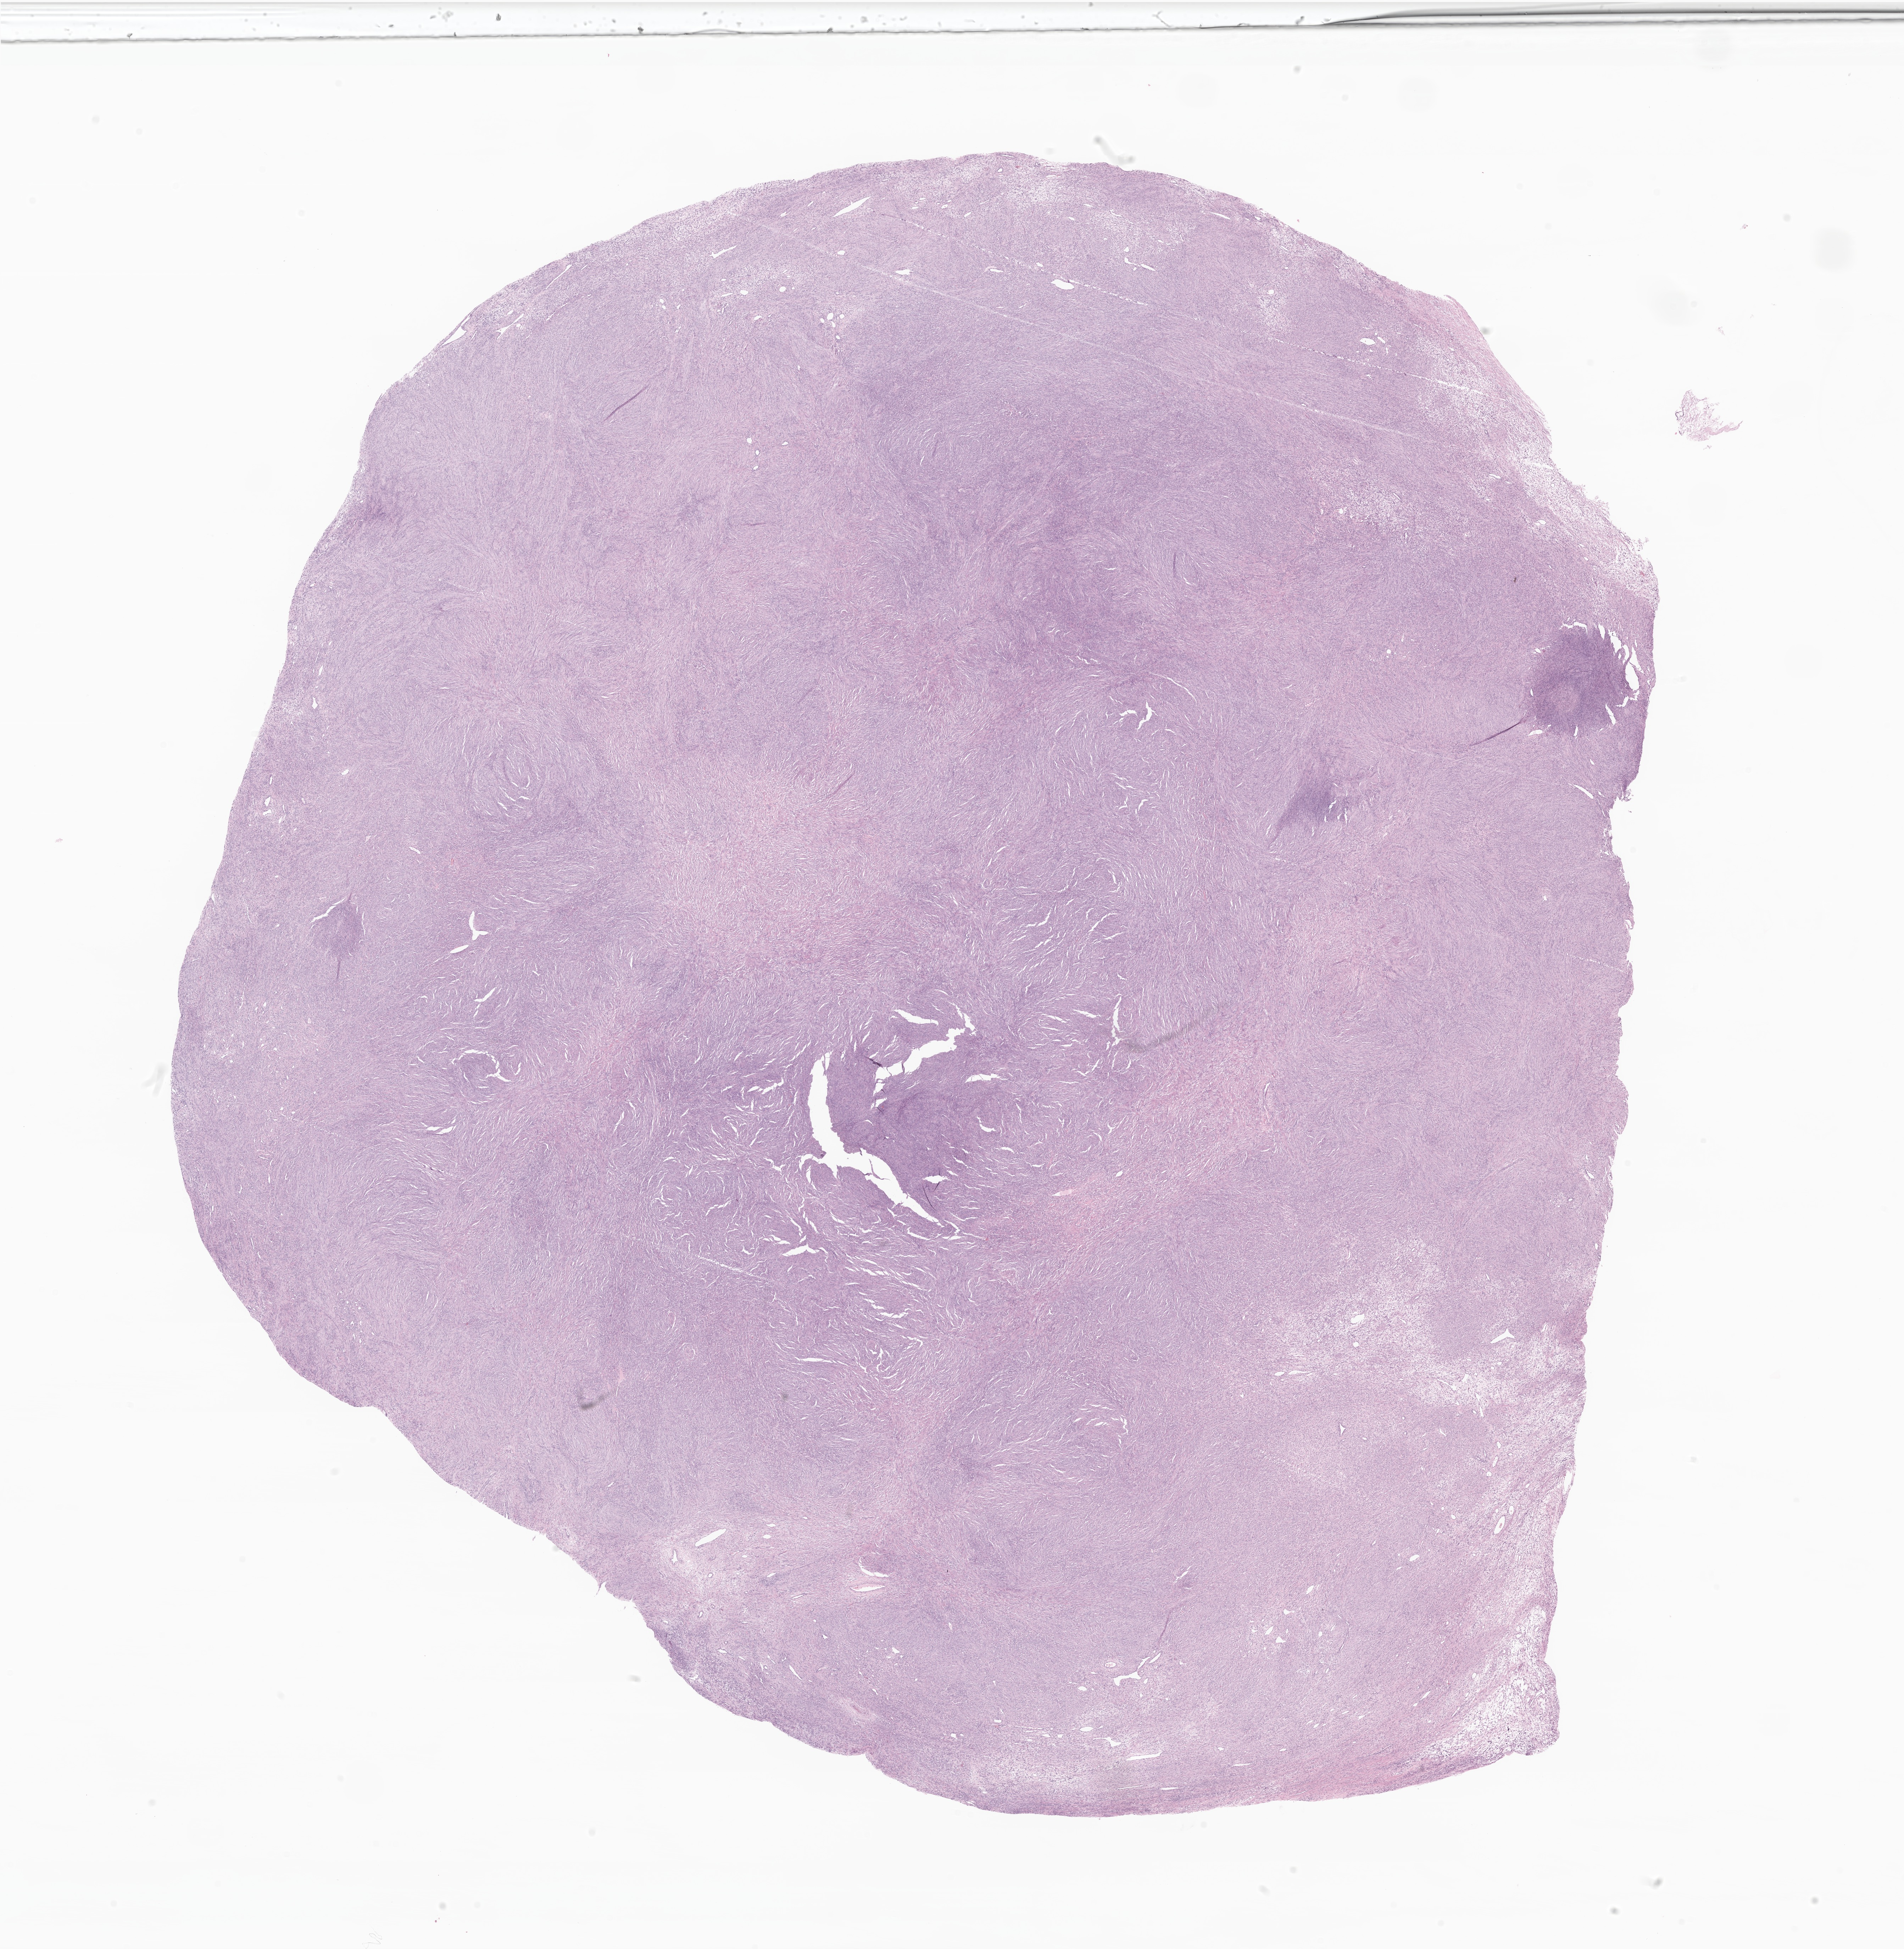
Digitized hematoxylin and eosin (H&E)-stained section of tumor tissue from the scrotum — shown as a low-resolution overview of the whole scanned area (about 22.6 x 23.2 mm); formalin-fixed paraffin-embedded section. Patient: male, age 142 months (11 years 10 months).
- diagnosis (ICD-O-3 morphology term): Sarcoma, NOS